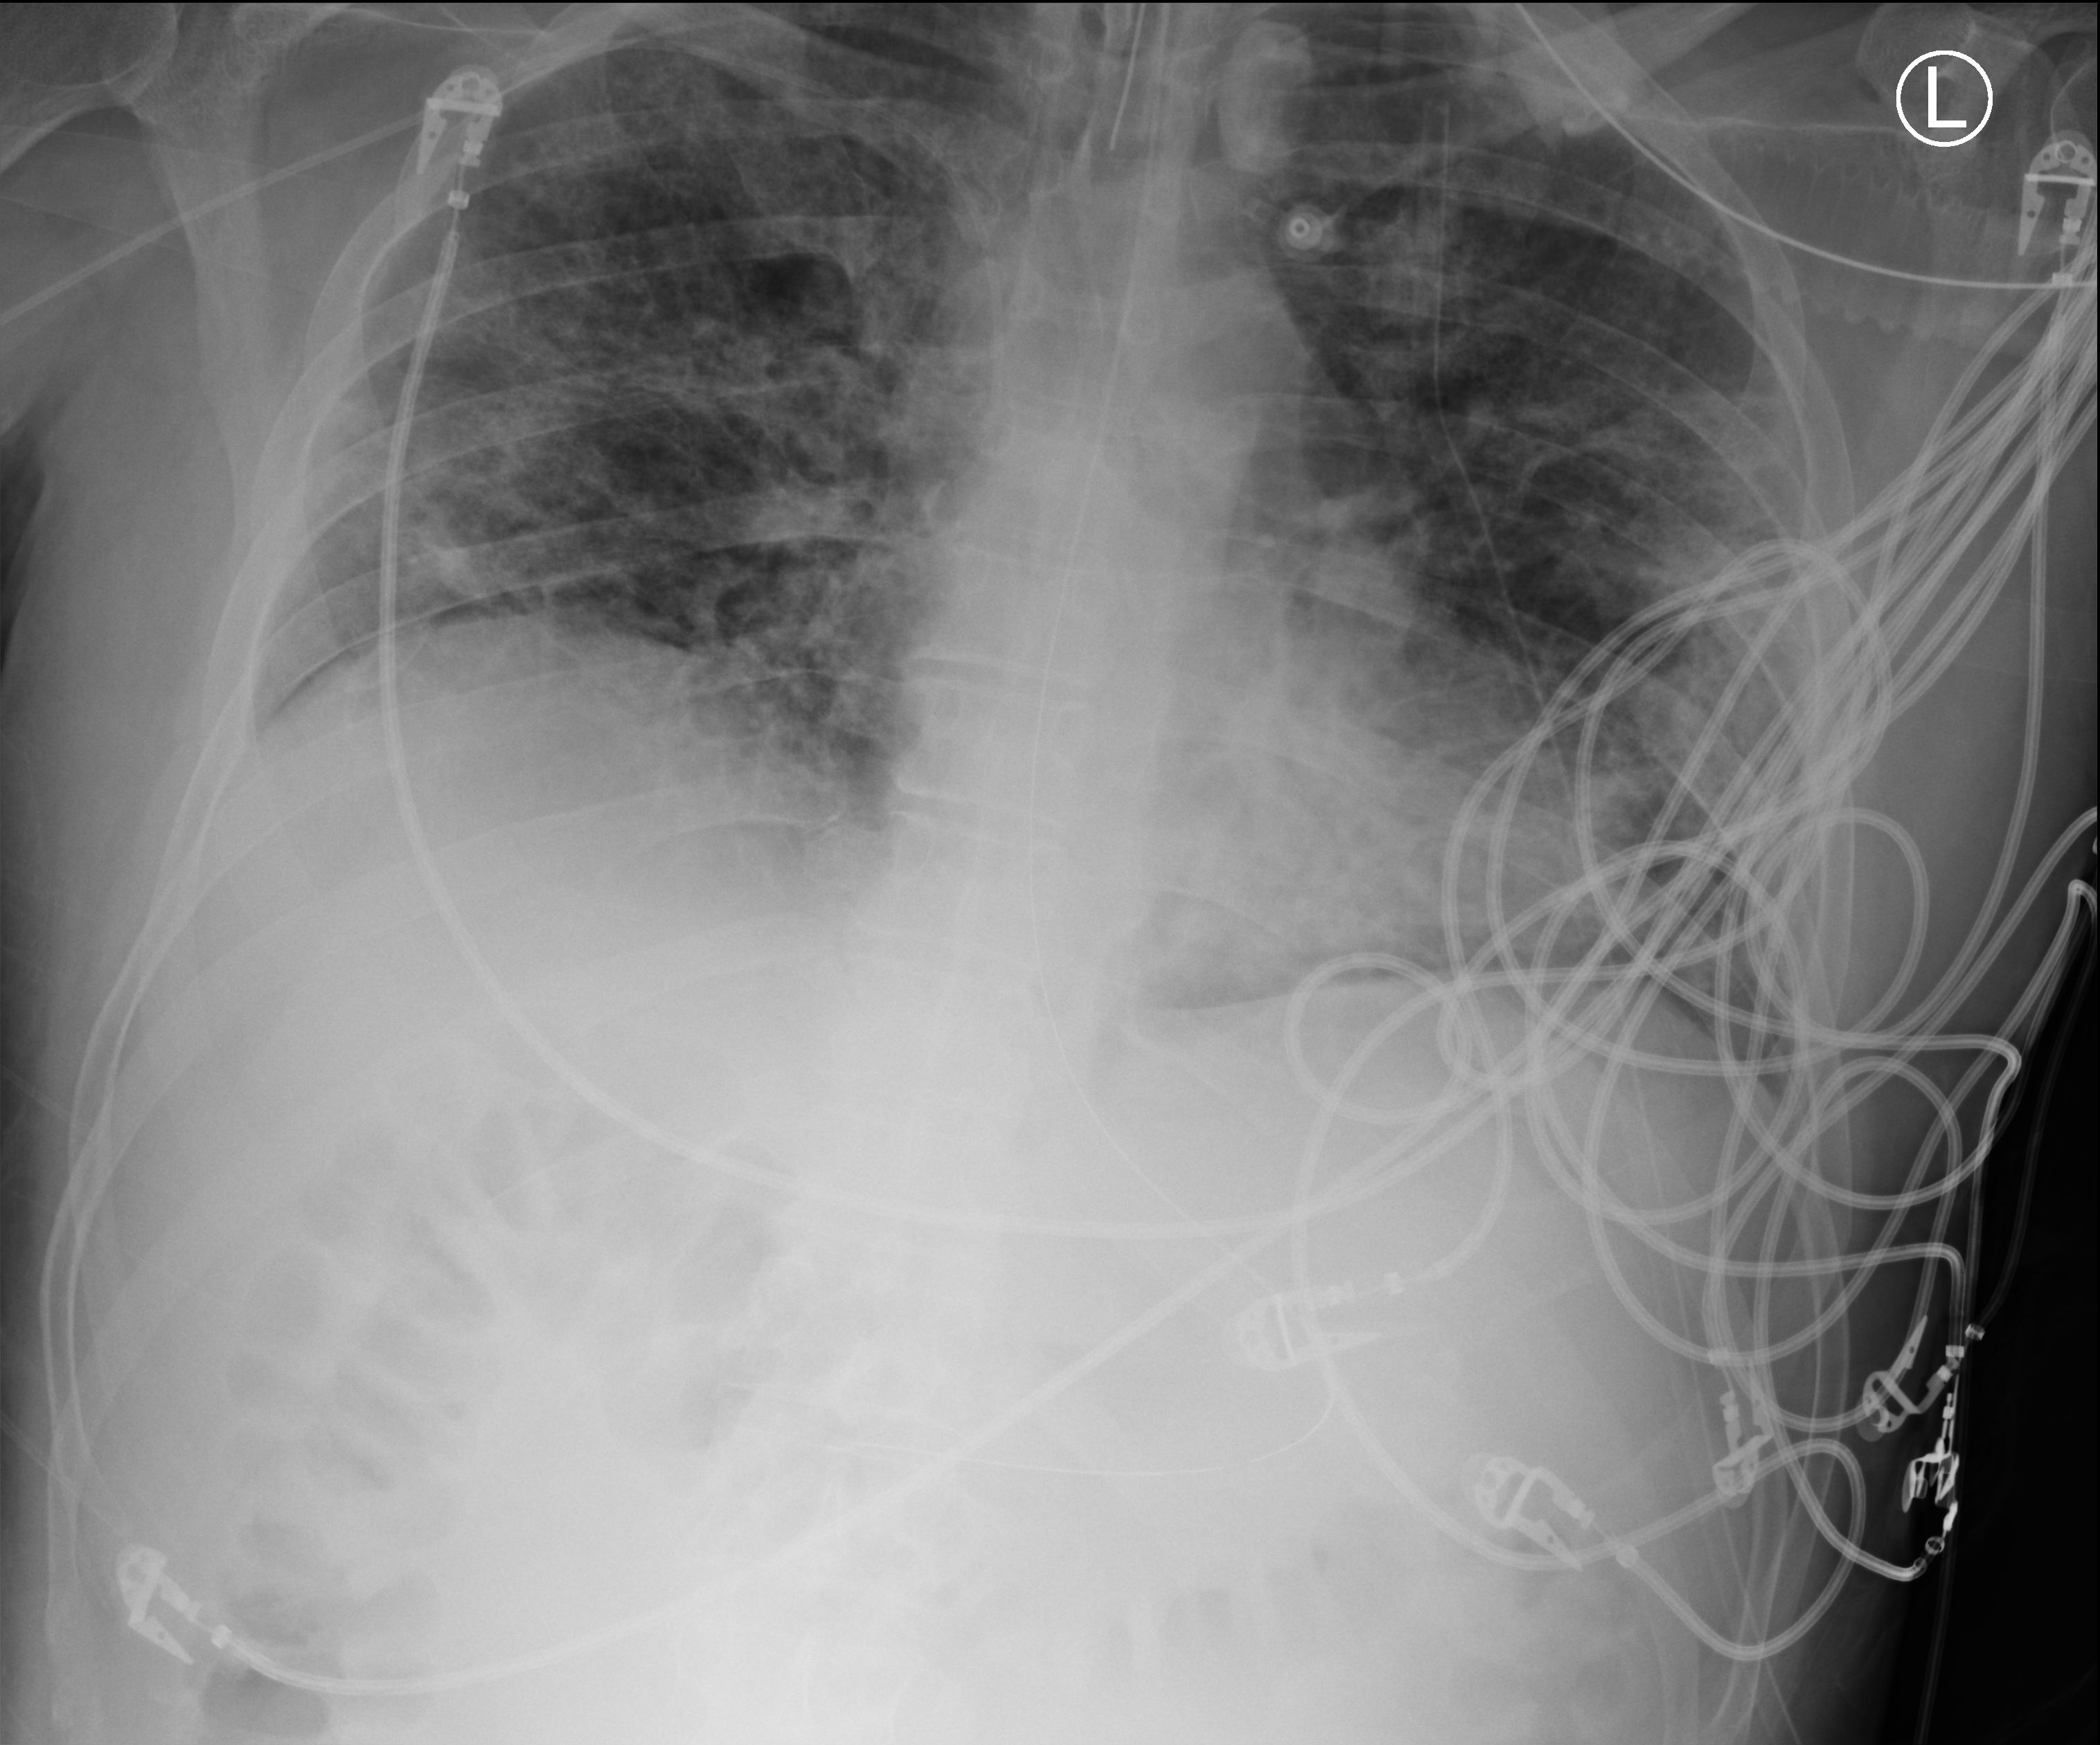
Portable chest radiograph, anteroposterior (AP) projection. Male patient hospitalised with COVID-19, age 18–59 years.
Hospital-stay facts (about this admission, not read from this image; timing relative to this image not recorded): mechanically ventilated during this hospital stay: yes; admitted to intensive care during this hospital stay: yes; length of hospital stay: 48 days.